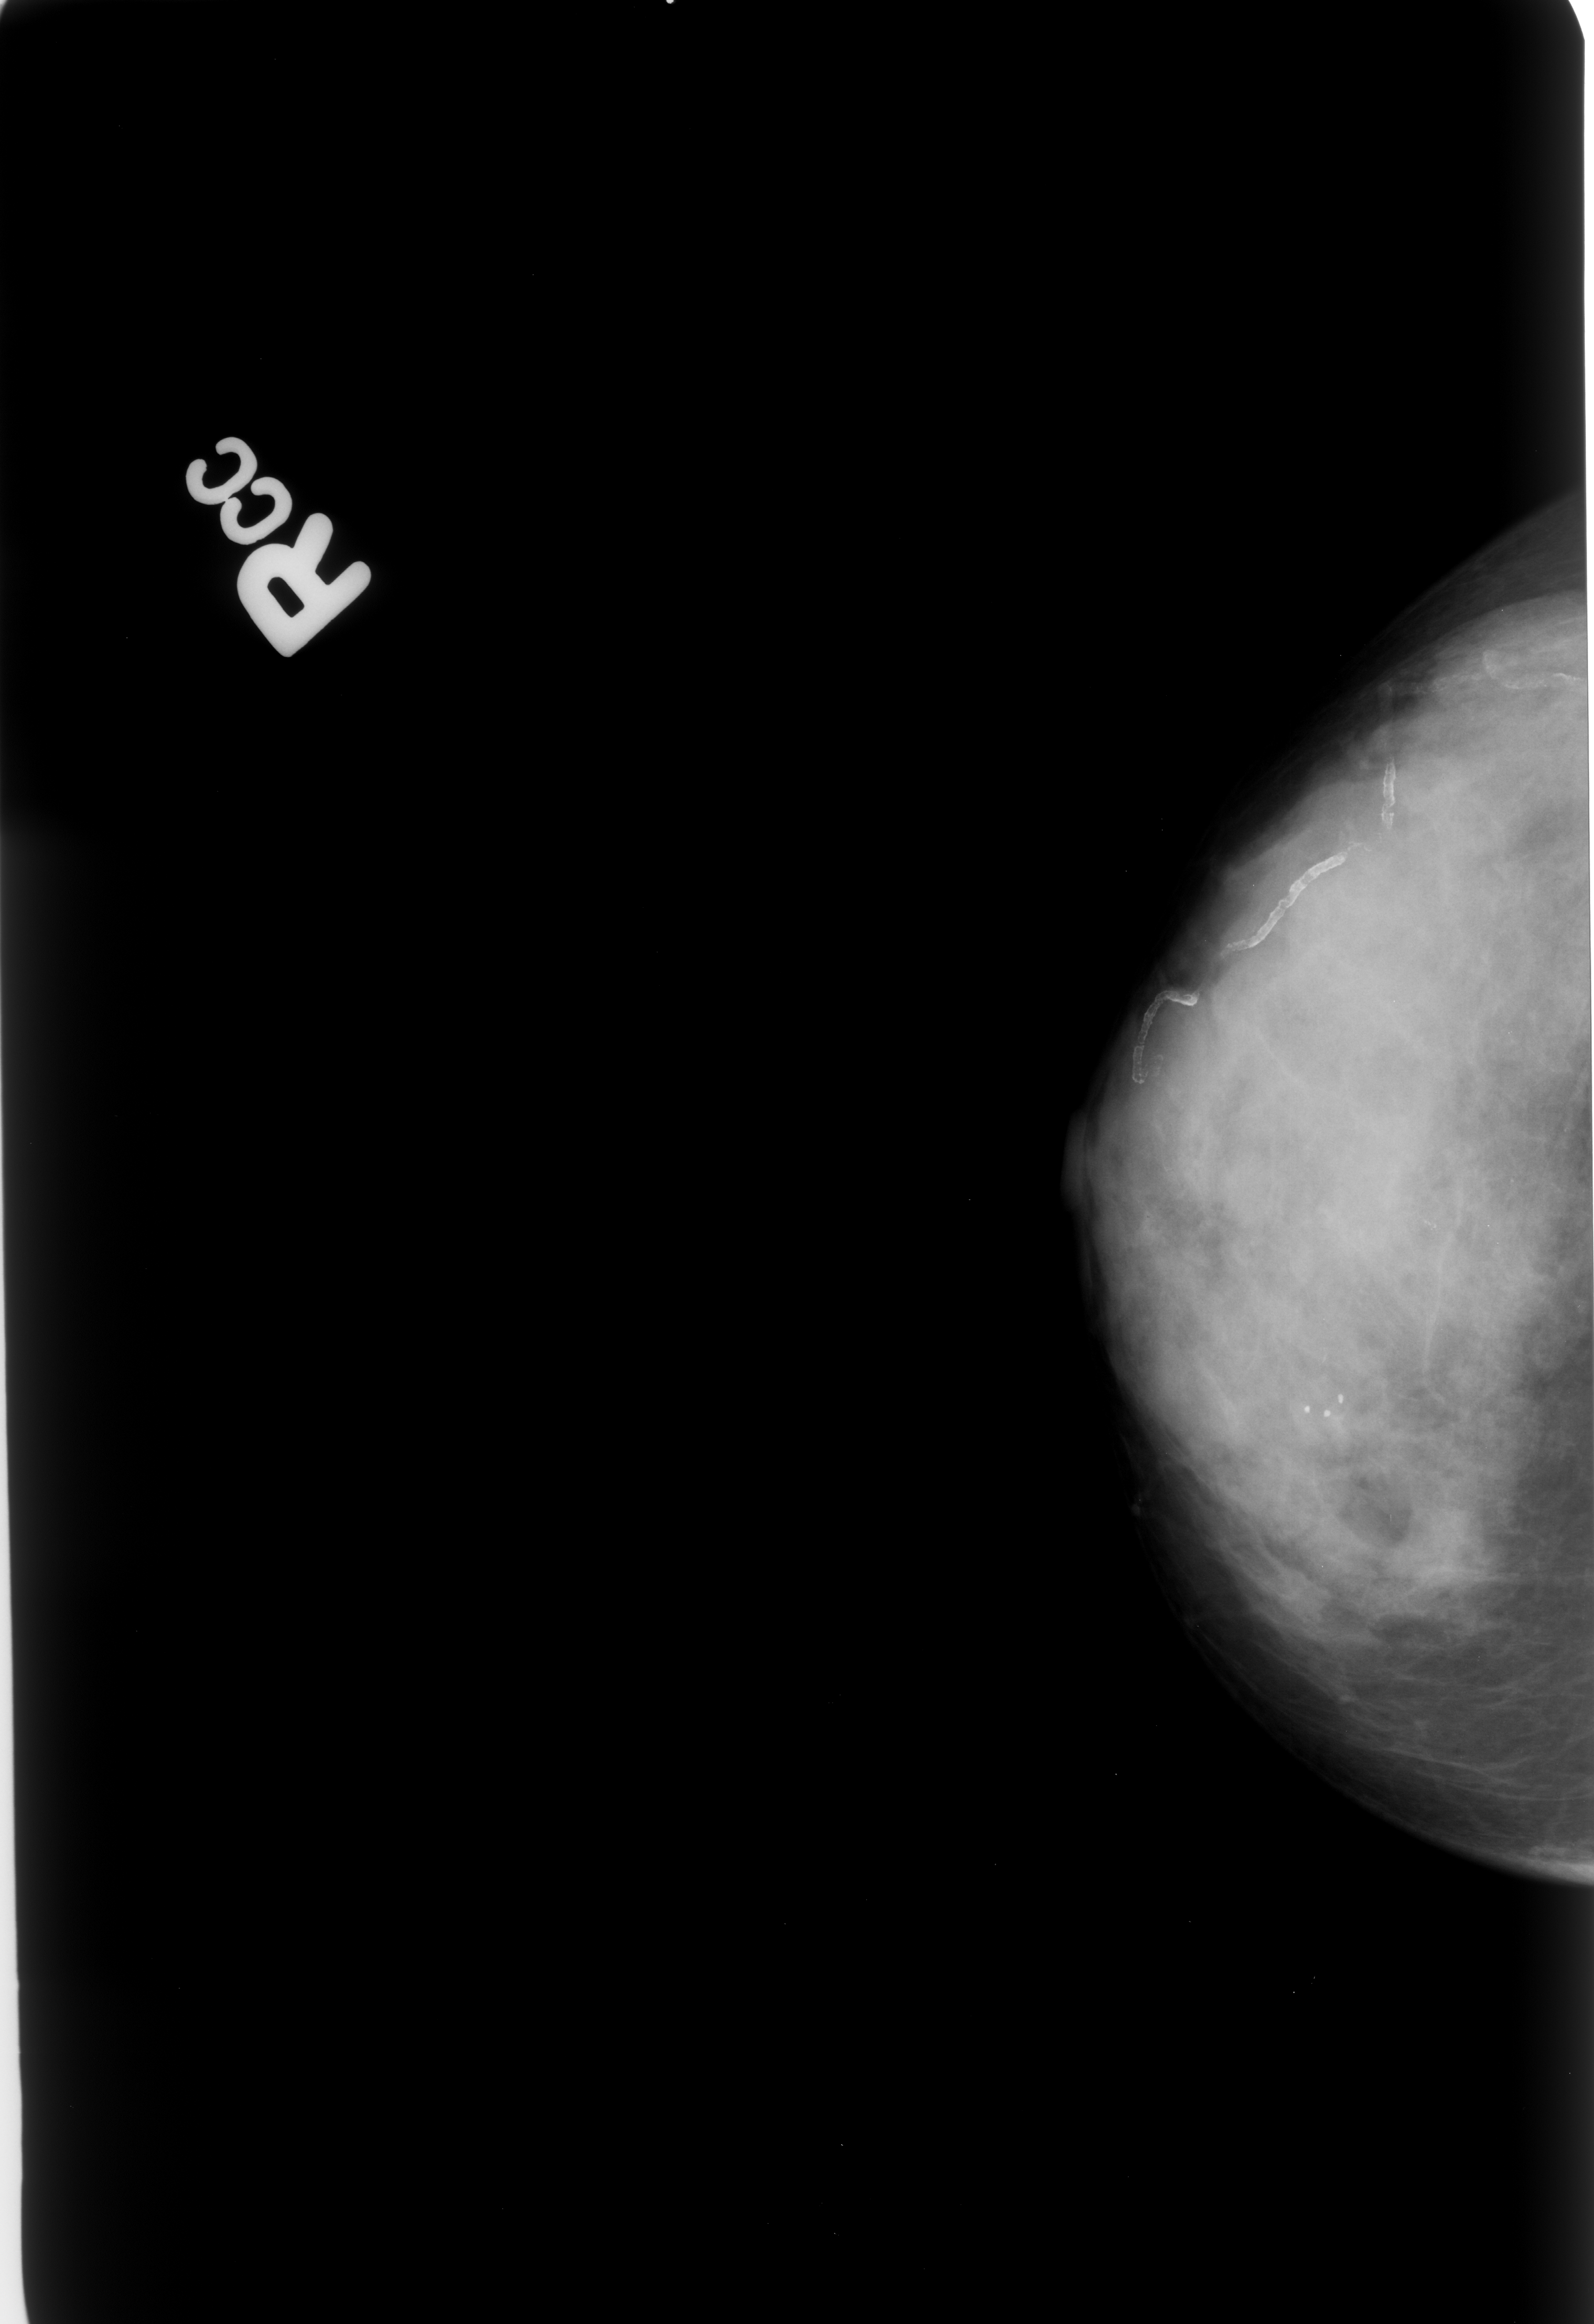
Digitized screen-film mammogram; right breast; craniocaudal (CC) view; BI-RADS breast density category 4 (scale 1–4).
- Calcifications, morphology pleomorphic, distribution clustered; BI-RADS assessment category 4; subtlety rating 3 on a 1 (subtle) to 5 (obvious) scale; pathology result (as recorded, not read from the image): benign.